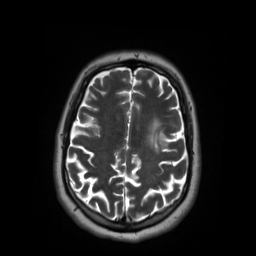
Brain MRI from a brain-tumour surgery series, one axial slice; slice 40 of 59 in the series (ordered by position); 256 × 256 image matrix, field of view 250 × 250 mm. From the clinical record (not read from this slice): histopathology: Oligodendroglioma; WHO grade: 2; IDH mutation: yes.
Annotated regions visible in this slice (manually delineated by an expert):
- tumour: bounding box (x1, y1, x2, y2) in pixels: (146, 122, 169, 153)